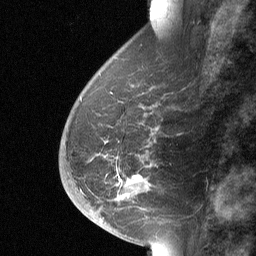
Breast MRI (dynamic contrast-enhanced), one sagittal slice; slice 24 of 64 in the series (ordered by position); dynamic contrast-enhanced study with each time point stored as its own series, time point 2 of 3 at this slice position (early post-contrast, ordered by acquisition time); 1.5 T; TE 4.8 ms, TR 27 ms; 2 mm slice thickness; 256 × 256 image matrix. Female patient, age 56 years. Case-level facts recorded for this patient, not image findings: setting: breast cancer imaged before/during neoadjuvant chemotherapy; receptor status: HER2-positive.
Annotated regions visible in this slice (semi-automatic segmentation, software-assisted and operator-edited):
- analysis volume of interest (the breast-tissue region the enhancement analysis was run in; not a lesion): bounding box (x1, y1, x2, y2) in pixels: (68, 83, 158, 214)
- tumour enhancement mask (voxels above the 90 % enhancement threshold inside the analysis volume of interest): (135, 177, 137, 179)